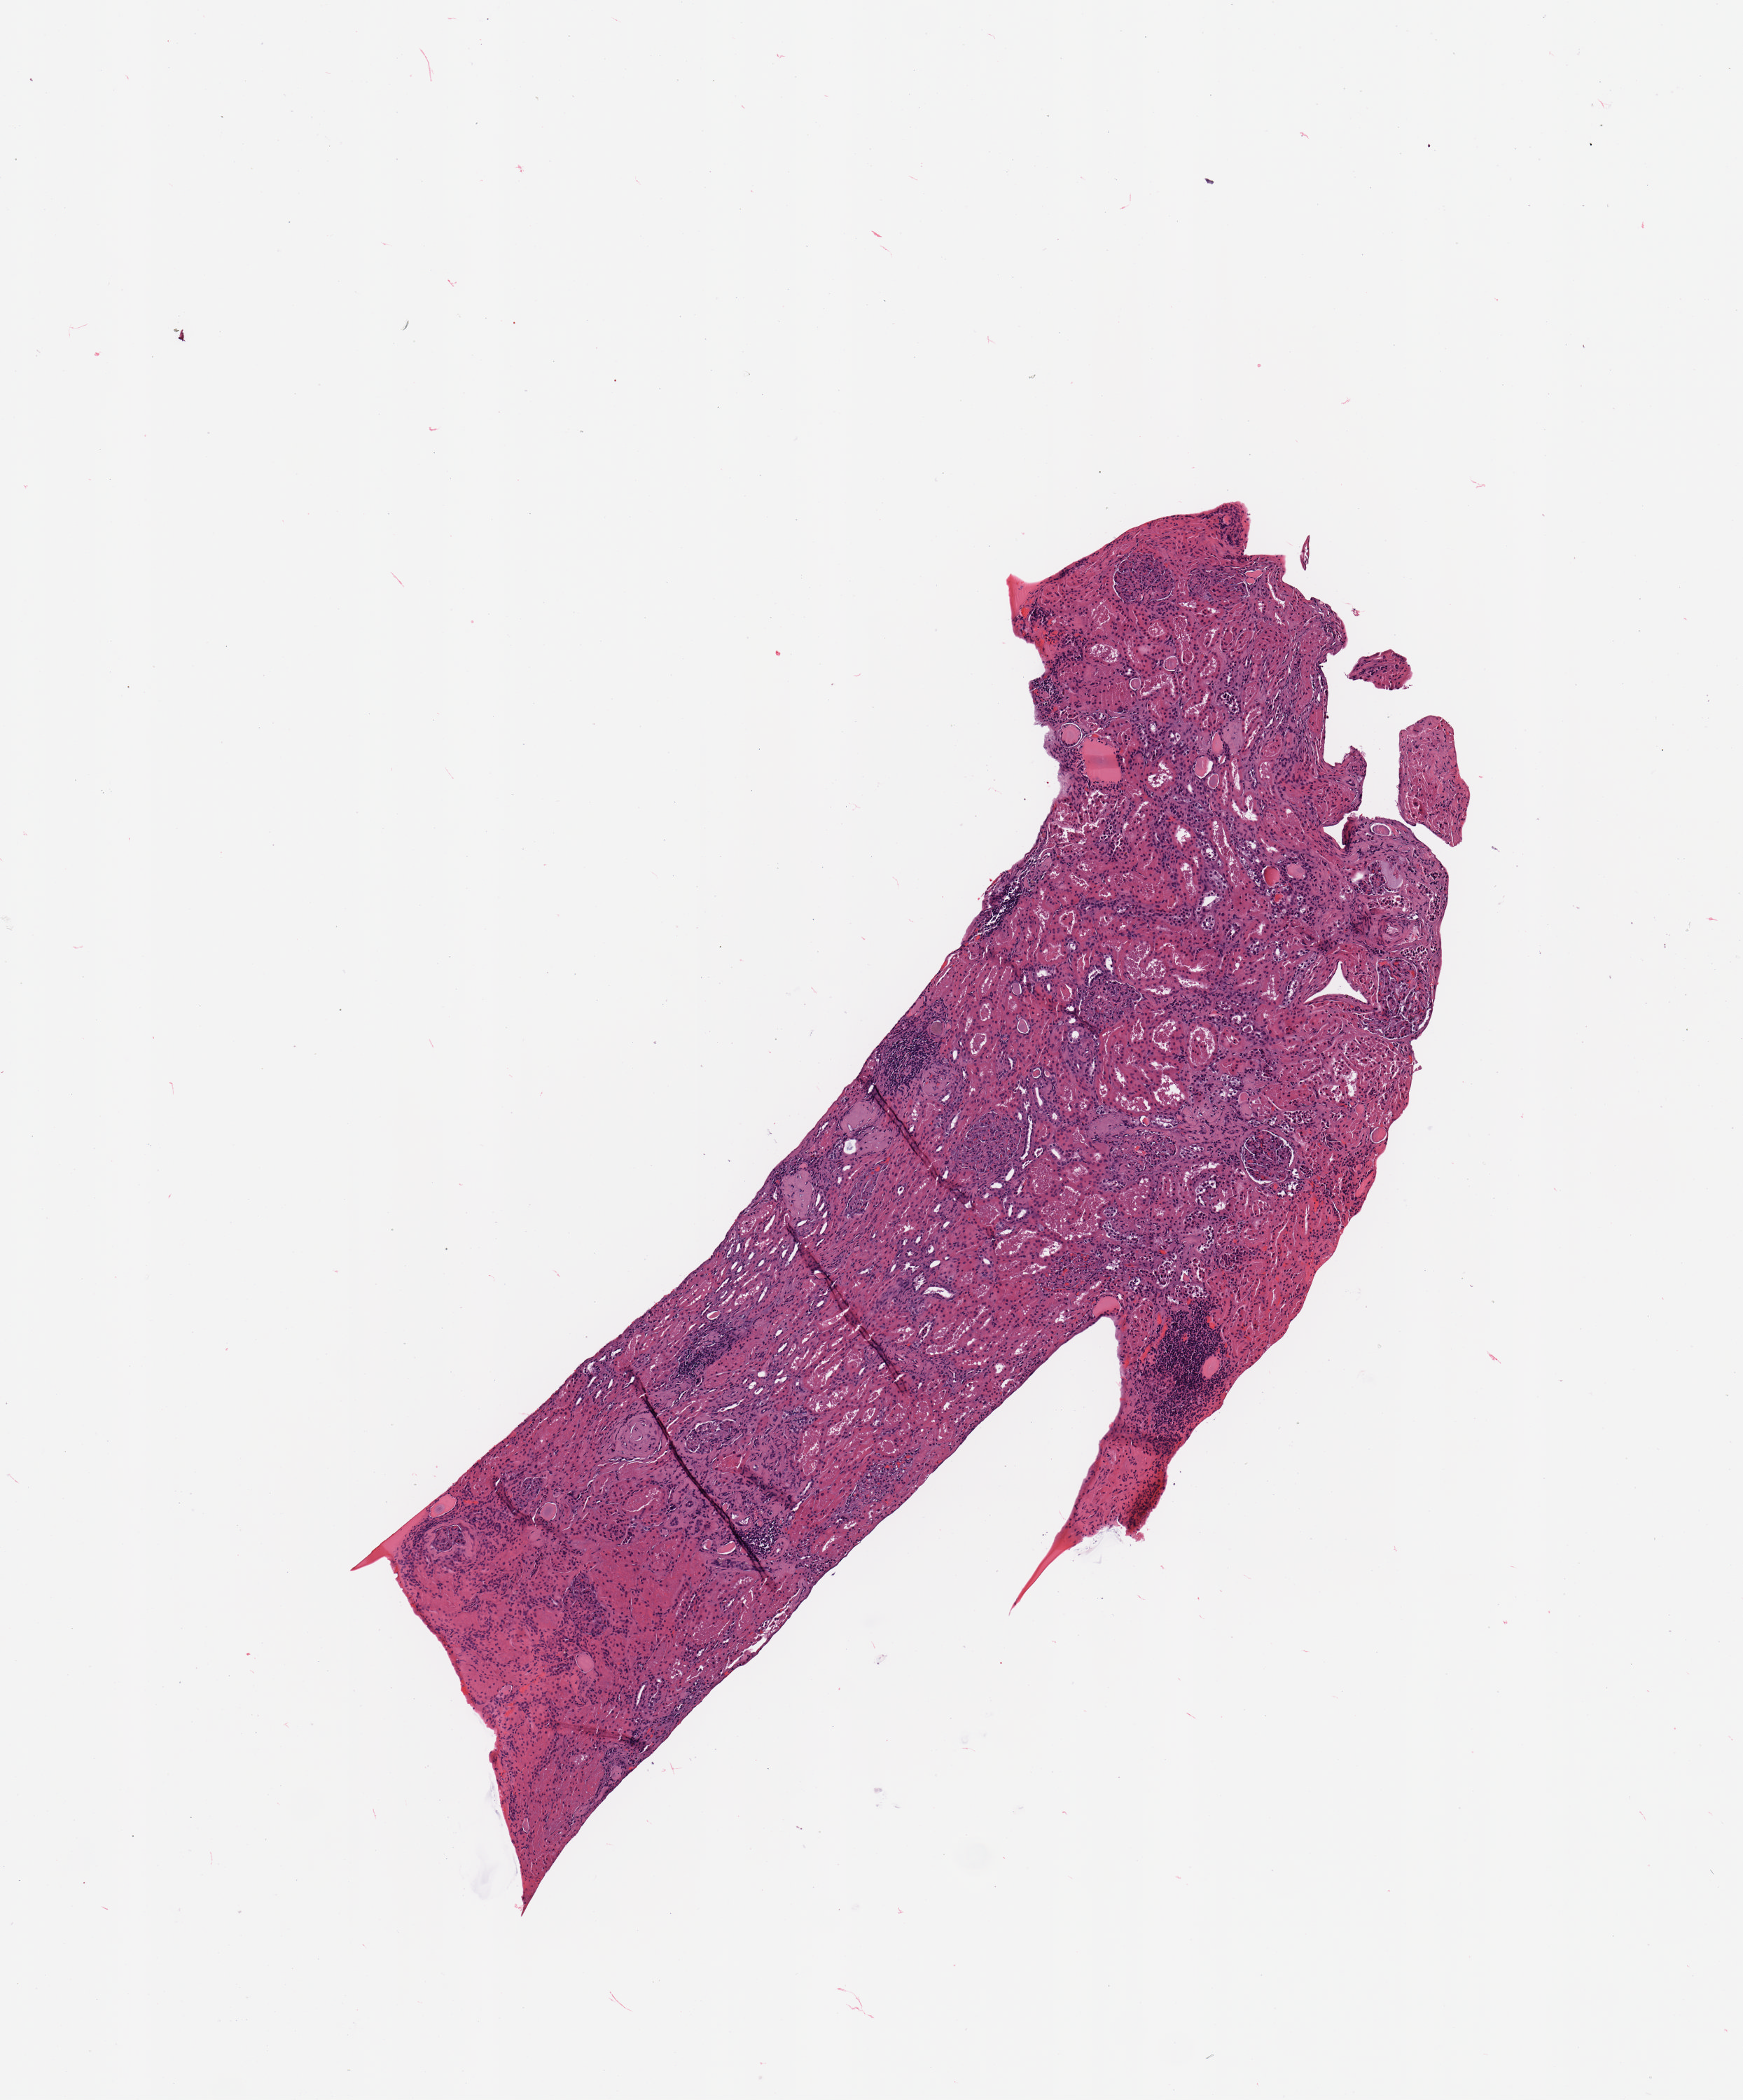
Whole-slide histology image, H&E-stained, low-resolution overview of the scanned area, about 4.9 x 5.9 mm (slide scanned at 20x); kidney, normal (non-tumour) tissue. Female, 76 y/o.
This section: normal (non-tumour) tissue from the same patient. Patient diagnosis: Renal cell carcinoma, NOS.